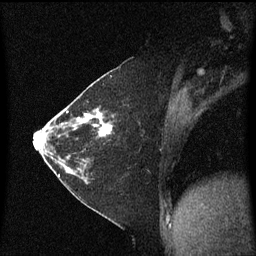
Breast MRI (dynamic contrast-enhanced), one sagittal slice. Slice 28 of 60 in the series (ordered by position). Dynamic contrast-enhanced series, image 2 of 3 at this slice position (ordered by acquisition). 1.5 T. TE 4.2 ms, TR 8.4 ms. 2 mm slice thickness. 256 × 256 image matrix, field of view 200 × 200 mm. Female patient, age 36 years. From the clinical record (not read from this slice): setting: breast cancer imaged before/during neoadjuvant chemotherapy; receptor status: HR-positive, HER2-negative.
Structures marked on this image (semi-automatic segmentation, software-assisted and operator-edited):
- analysis volume of interest (the breast-tissue region the enhancement analysis was run in; not a lesion): bounding box (x1, y1, x2, y2) in pixels: (66, 102, 115, 179)
- tumour enhancement mask (voxels above the 70 % enhancement threshold inside the analysis volume of interest): (77, 110, 113, 137)